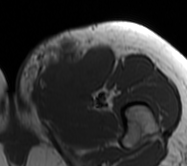
MRI of an extremity soft-tissue mass, one axial slice. Slice 20 of 62 in the series (ordered by position). MR volume resampled by the dataset authors to the PET/CT grid (not the native acquisition matrix). 3.27 mm slice thickness. 187 × 166 image matrix, field of view 183 × 162 mm. Female patient. Case-level facts recorded for this patient, not image findings: histological type: leiomyosarcoma; grade: high; site of the primary tumour: groin.
Annotated regions visible in this slice (expert contour drawn on MRI and transferred to this co-registered scan by the dataset authors):
- gross tumour volume including surrounding oedema: bounding box (x1, y1, x2, y2) in pixels: (16, 35, 113, 109)
- gross tumour volume (mass): (39, 47, 113, 98)